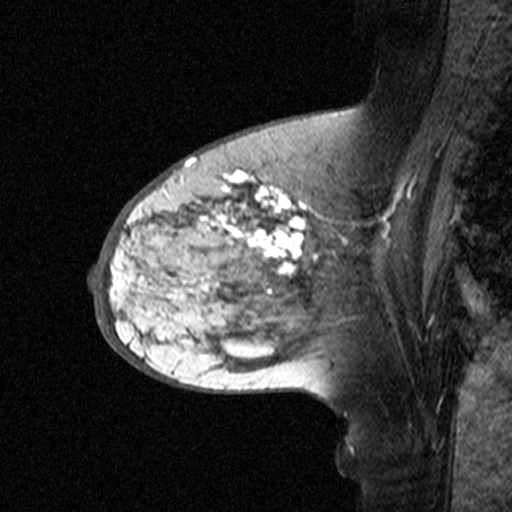
Breast MRI (dynamic contrast-enhanced), one sagittal slice; slice 24 of 44 in the series (ordered by position); dynamic contrast-enhanced study with each time point stored as its own series, time point 2 of 3 at this slice position (early post-contrast, ordered by acquisition time); 1.5 T; TE 4.5 ms, TR 11 ms; 3 mm slice thickness; 512 × 512 image matrix. Patient: female, 65 years. Case-level facts recorded for this patient, not image findings: setting: breast cancer imaged before/during neoadjuvant chemotherapy; receptor status: HER2-positive.
Annotated regions visible in this slice (semi-automatic segmentation, software-assisted and operator-edited):
- analysis volume of interest (the breast-tissue region the enhancement analysis was run in; not a lesion): bounding box [x1, y1, x2, y2] px = [160, 172, 329, 345]
- tumour enhancement mask (voxels above the 90 % enhancement threshold inside the analysis volume of interest): [173, 172, 319, 283]